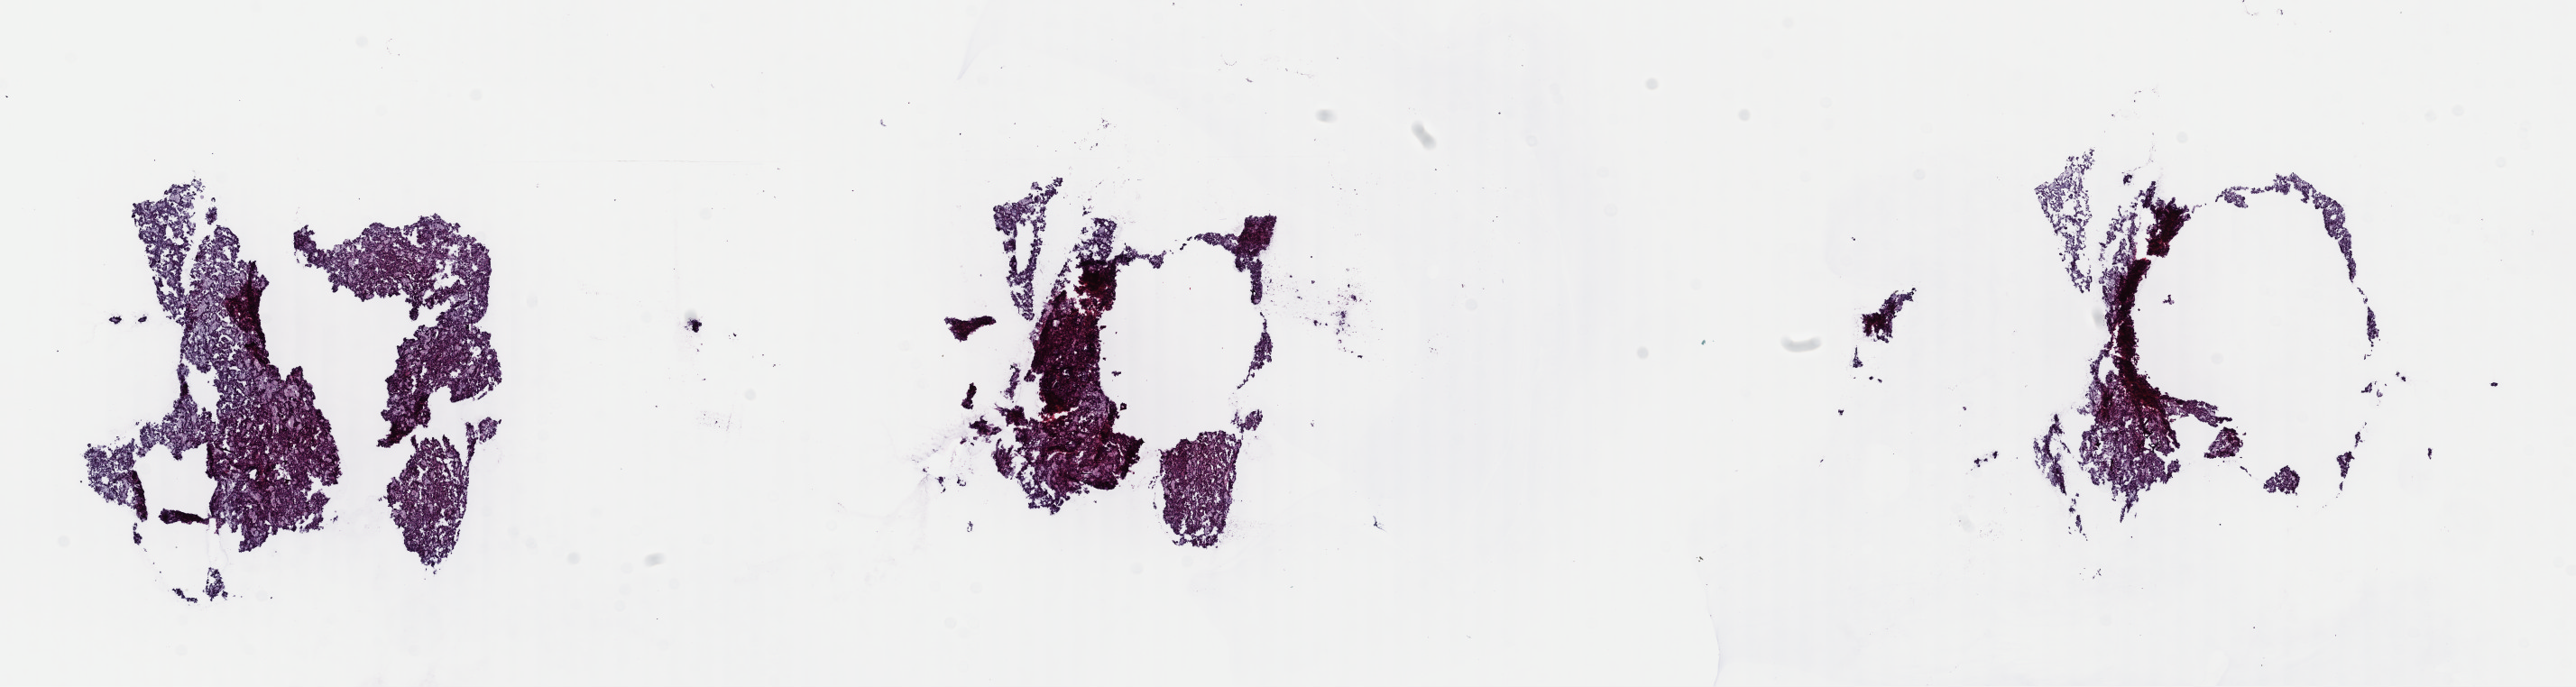
H&E-stained whole-slide image, shown as a low-resolution overview of the whole scanned area (about 22.5 x 6.0 mm, acquisition: 40x scan). Frozen section from the top of the tissue portion. Sample: primary tumour, kidney. Patient: male, age at initial diagnosis 50 years. Pathologist review of this section (percent, as recorded): tumour cells 100%, tumour nuclei 80%, normal cells 0%, stromal cells 0%, necrosis 0%. Infiltration values recorded for this section: lymphocyte infiltration 1%, monocyte infiltration 3%, neutrophil infiltration 0%.
Laterality: right. Histologic diagnosis: Papillary adenocarcinoma, NOS. AJCC pathologic stage: I (7th edition). TNM: T1b NX MX.